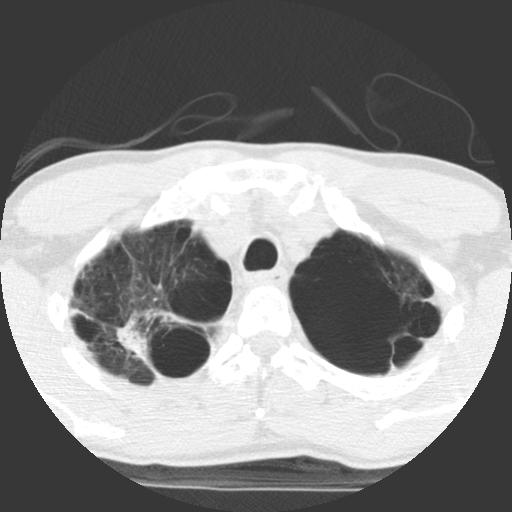
Low-dose screening chest CT, axial slice; baseline screening round; lung window (W 1500 / L -600 HU); 2.5 mm slice thickness; 140 kVp. Male participant, aged 62 years at enrolment. Current smoker at enrolment.
Lesion marked by an expert reader, bounding box [x1, y1, x2, y2] px = [111, 305, 214, 387]. Screening reader's record for this exam: no non-calcified nodule ≥4 mm recorded. Official screen result: negative screen, minor abnormalities not suspicious for lung cancer. Lung cancer was diagnosed 357 days after this screen (after the second annual screen): non-small cell carcinoma, right upper lobe, poorly differentiated (G3), stage IA (AJCC 6th edition), 70 mm at pathology.